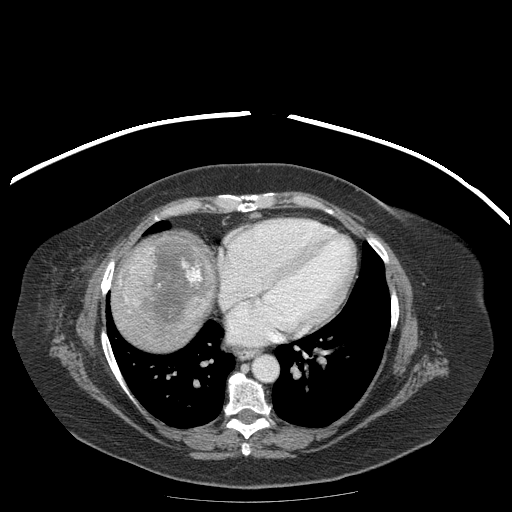
Contrast-enhanced abdominal CT (liver protocol), one axial slice; position 175 of 204 along the scan axis; reconstruction kernel STANDARD; soft-tissue window (W 400 / L 40 HU); 2.5 mm slice thickness; 512 × 512 image matrix, field of view 440 × 440 mm. Case-level facts recorded for this patient, not image findings: diagnosis: hepatocellular carcinoma (patient treated with transarterial chemoembolisation; whether this scan precedes or follows treatment is not stated here); TNM stage (as recorded): Stage-IIIB.
Annotated regions visible in this slice (semi-automatic segmentation, software-assisted and operator-edited):
- liver parenchyma outside the tumour (the mass and vessels are separate outlines, so this box may not span the whole liver): bounding box [x1, y1, x2, y2] px = [112, 234, 212, 350]
- mass: [119, 237, 212, 326]